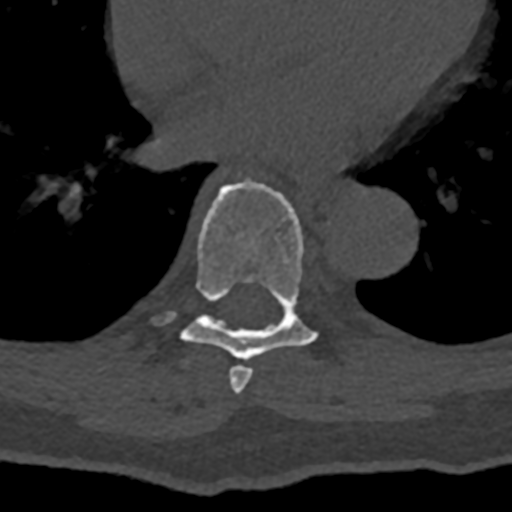
CT including the spine, one axial slice; bone window (W 1800 / L 400 HU); 512 × 512 image matrix. Male patient, age 74 years. Case-level facts recorded for this patient, not image findings: primary cancer: renal; vertebrae with lytic lesions (as recorded): T10, L1, L2, L3, L4, L5.
Outlined on this slice (semi-automatically segmented with operator editing):
- T7 vertebra: bounding box (x1, y1, x2, y2) in pixels: (229, 365, 253, 394)
- T8 vertebra: (154, 180, 330, 360)